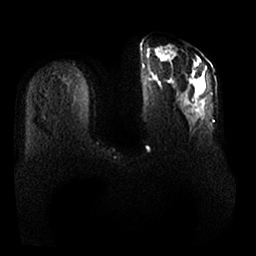
Breast MRI, one axial slice; position 6 of 25 along the scan axis; diffusion-weighted series; image 2 of 4 stored at this slice position (different b-values; order by instance number); 1.5 T; 256 × 256 image matrix, field of view 380 × 380 mm. Female patient.
Outlined on this slice (outlined manually by an expert reader):
- tumour on diffusion-weighted imaging: bounding box (x1, y1, x2, y2) in pixels: (157, 53, 204, 87)